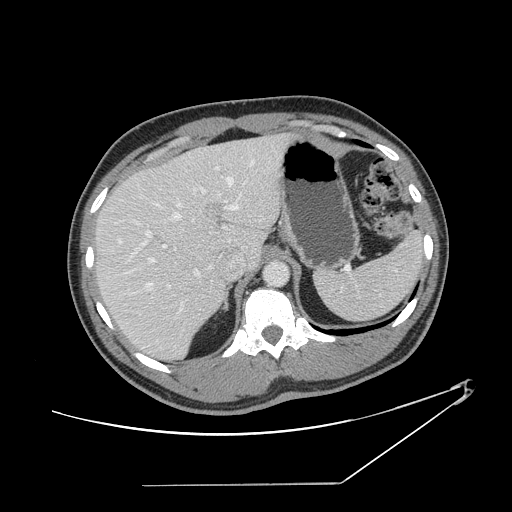
Contrast-enhanced abdominal CT, one axial slice; position 103 of 152 along the scan axis; intravenous contrast given; soft-tissue window (W 400 / L 40 HU); 512 × 512 image matrix, field of view 432 × 432 mm. Male patient, age 45 years. From the clinical record (not read from this slice): diagnosis: colorectal cancer liver metastases, imaged before liver resection; multiple liver metastases: no; largest metastasis: 1 cm; disease in both lobes: no.
Annotated regions visible in this slice (expert manual segmentation):
- hepatic veins: box from (x=111, y=158) to (x=255, y=313) px
- liver: (x=97, y=136)–(x=289, y=359)
- planned liver remnant (the part of the liver to remain after resection): (x=97, y=154)–(x=233, y=359)
- portal vein (with intrahepatic branches): (x=141, y=167)–(x=239, y=324)